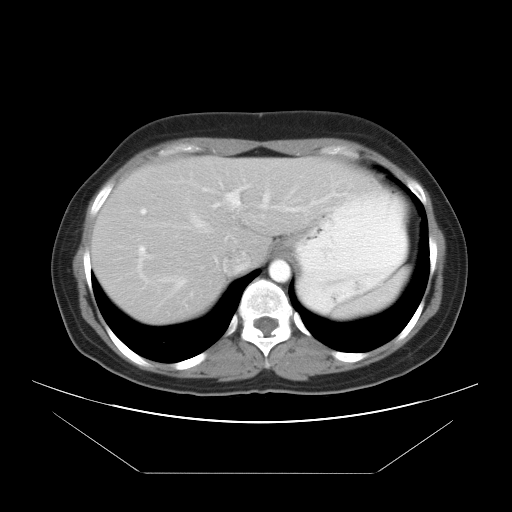
Contrast-enhanced abdominal CT, one axial slice; position 29 of 34 along the scan axis; intravenous contrast given; soft-tissue window (W 400 / L 40 HU); 7.5 mm slice thickness; 512 × 512 image matrix, field of view 410 × 410 mm. Female patient, age 38 years. Case-level facts recorded for this patient, not image findings: diagnosis: colorectal cancer liver metastases, imaged before liver resection; multiple liver metastases: yes; largest metastasis: 3.1 cm; chemotherapy before resection: no.
Outlined on this slice (outlined manually by an expert reader):
- hepatic veins: bounding box [x1, y1, x2, y2] px = [141, 196, 269, 297]
- liver: [91, 157, 369, 326]
- planned liver remnant (the part of the liver to remain after resection): [200, 157, 368, 264]
- portal vein (with intrahepatic branches): [140, 186, 340, 254]